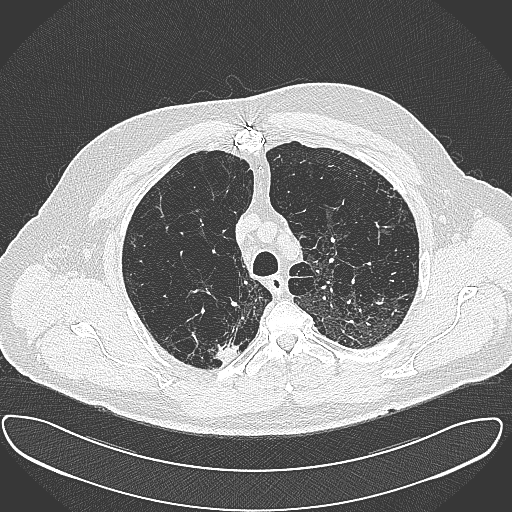
Low-dose screening chest CT, axial slice; baseline screening round; lung window (W 1500 / L -600 HU); 512 × 512 image matrix. Male participant, aged 60 years at enrolment.
• Expert reader's lesion annotation, box from (x=201, y=328) to (x=241, y=364) px.
• Reader record for this screening exam (exam-level; its link to the box is not recorded): non-calcified nodule or mass ≥4 mm, right upper lobe, 15 × 25 mm, spiculated (stellate) margins, soft tissue attenuation.
• Later outcome: lung cancer diagnosed 32 days after this screen — carcinoma, NOS, right upper lobe, moderately differentiated (G2), stage IB (AJCC 6th edition), 35 mm at pathology.